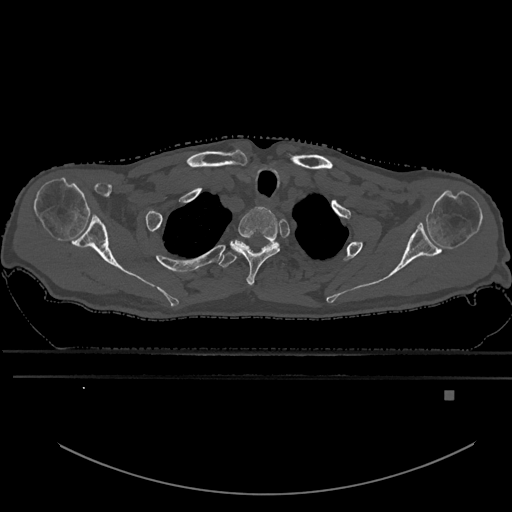
CT including the spine, one axial slice. Position 525 of 969 along the scan axis. Bone window (W 1800 / L 400 HU). 0.5 mm slice thickness. 512 × 512 image matrix, field of view 456 × 456 mm. Male patient, age 82 years. Case-level facts recorded for this patient, not image findings: primary cancer: prostate; vertebrae with lytic lesions (as recorded): T11, T9, T8, T2.
Annotated regions visible in this slice (semi-automatic segmentation, software-assisted and operator-edited):
- T1 vertebra: bounding box <231,207,281,286> (left, top, right, bottom; pixels)
- T2 vertebra: <219,238,280,267>